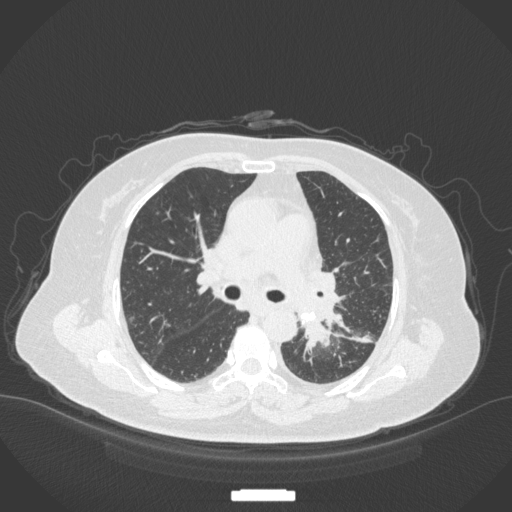
Chest CT, one axial slice. Slice 212 of 328 in the series (ordered by position). Reconstruction kernel B31f. Lung window (W 1500 / L -600 HU). 512 × 512 image matrix, field of view 400 × 400 mm. Patient: female, 69 years. From the clinical record (not read from this slice): clinical TNM (as recorded): T2b N3 M1.
Annotated regions visible in this slice (rectangle marked by the reading radiologist):
- lung tumour (recorded histology: adenocarcinoma): box from (x=288, y=308) to (x=330, y=360) px